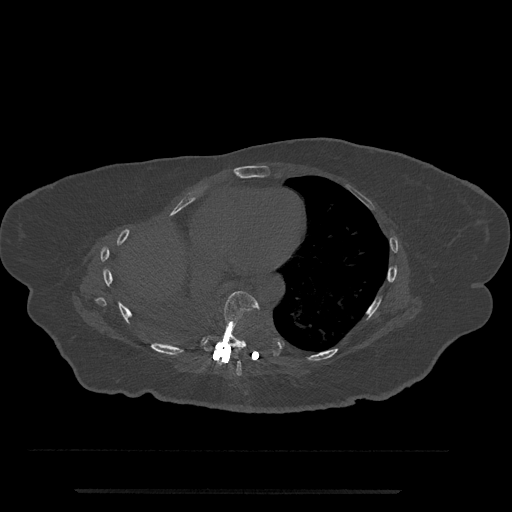
CT including the spine, one axial slice. Slice 397 of 797 in the series (ordered by position). Bone window (W 1800 / L 400 HU). 0.5 mm slice thickness. 512 × 512 image matrix, field of view 440 × 440 mm. Patient: female, 51 years. From the clinical record (not read from this slice): primary cancer: neuro; vertebrae with lytic lesions (as recorded): T8.
Structures marked on this image (semi-automatic segmentation, software-assisted and operator-edited):
- T7 vertebra: bounding box (x1, y1, x2, y2) in pixels: (232, 361, 242, 376)
- T8 vertebra: (201, 291, 260, 352)